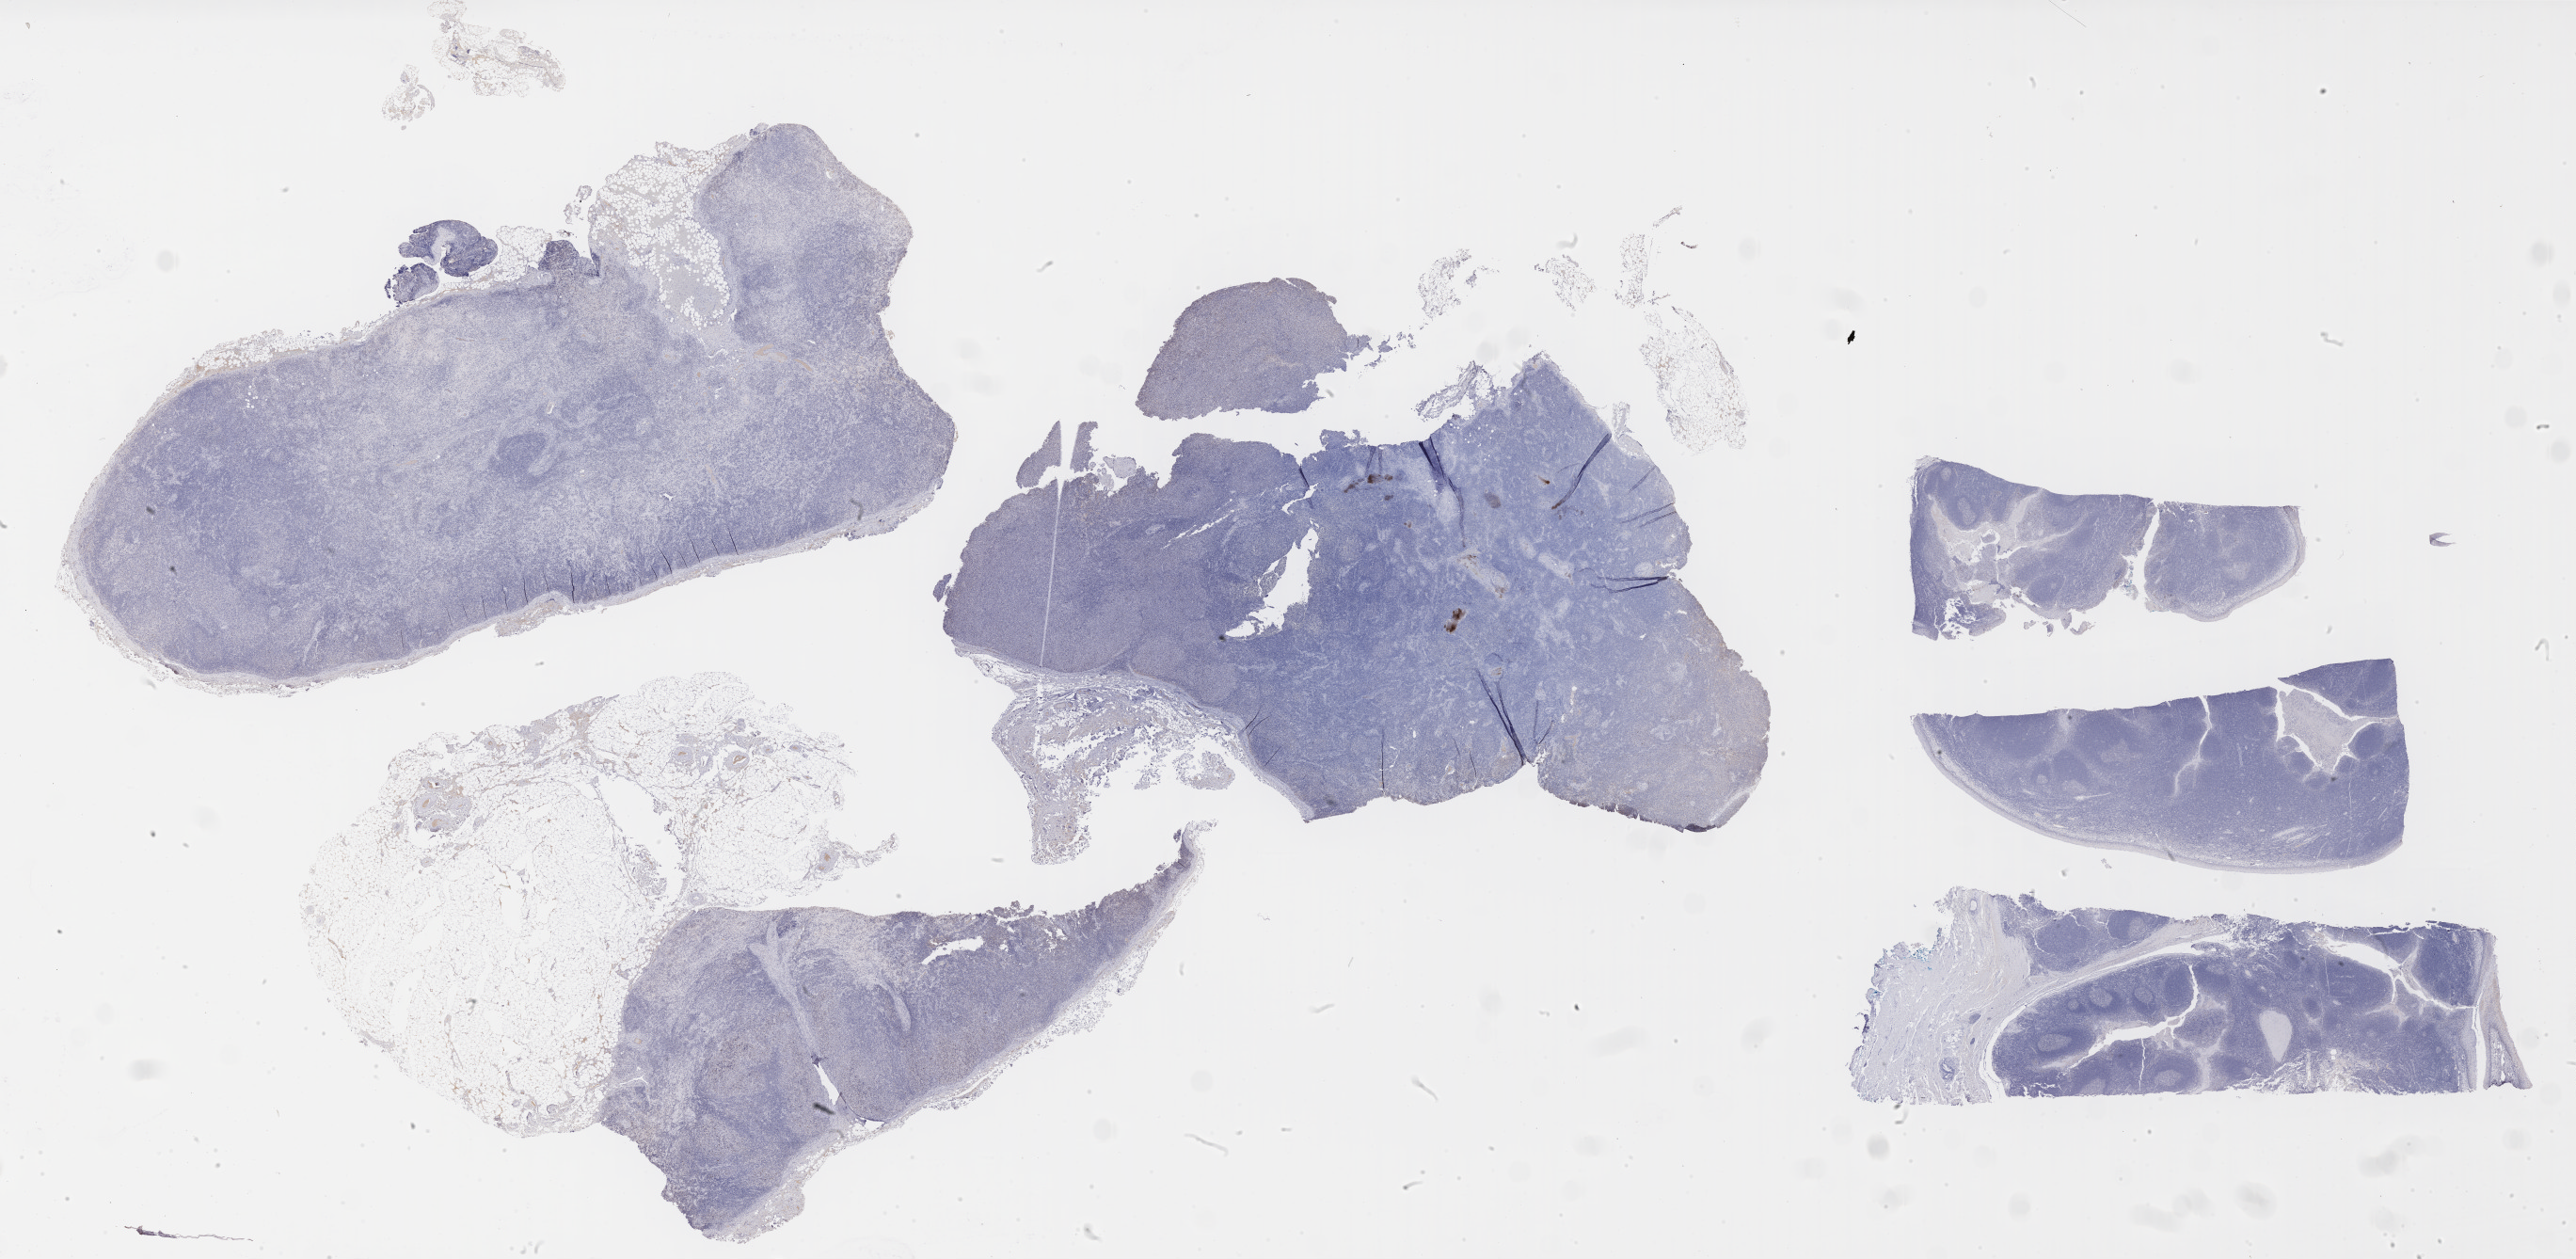
IHC for p53, whole-slide image — shown as a low-resolution overview of the whole scanned area (about 44.3 x 21.6 mm), specimen: tumor tissue, anatomic site: lymph node. Male patient, age 56 years.
Histologic diagnosis: Diffuse large B-cell lymphoma, NOS.